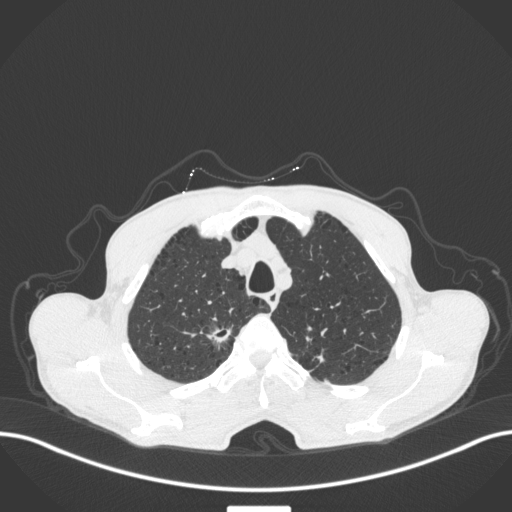
Chest CT, one axial slice. 120 kVp. Lung window (W 1500 / L -600 HU). 512 × 512 image matrix. Male patient, age 70 years. Case-level facts recorded for this patient, not image findings: clinical TNM (as recorded): T1a N0 M0; histopathological grade: G1-2.
Structures marked on this image (bounding box drawn by a radiologist):
- lung tumour (recorded histology: adenocarcinoma): bounding box <204,318,237,347> (left, top, right, bottom; pixels)